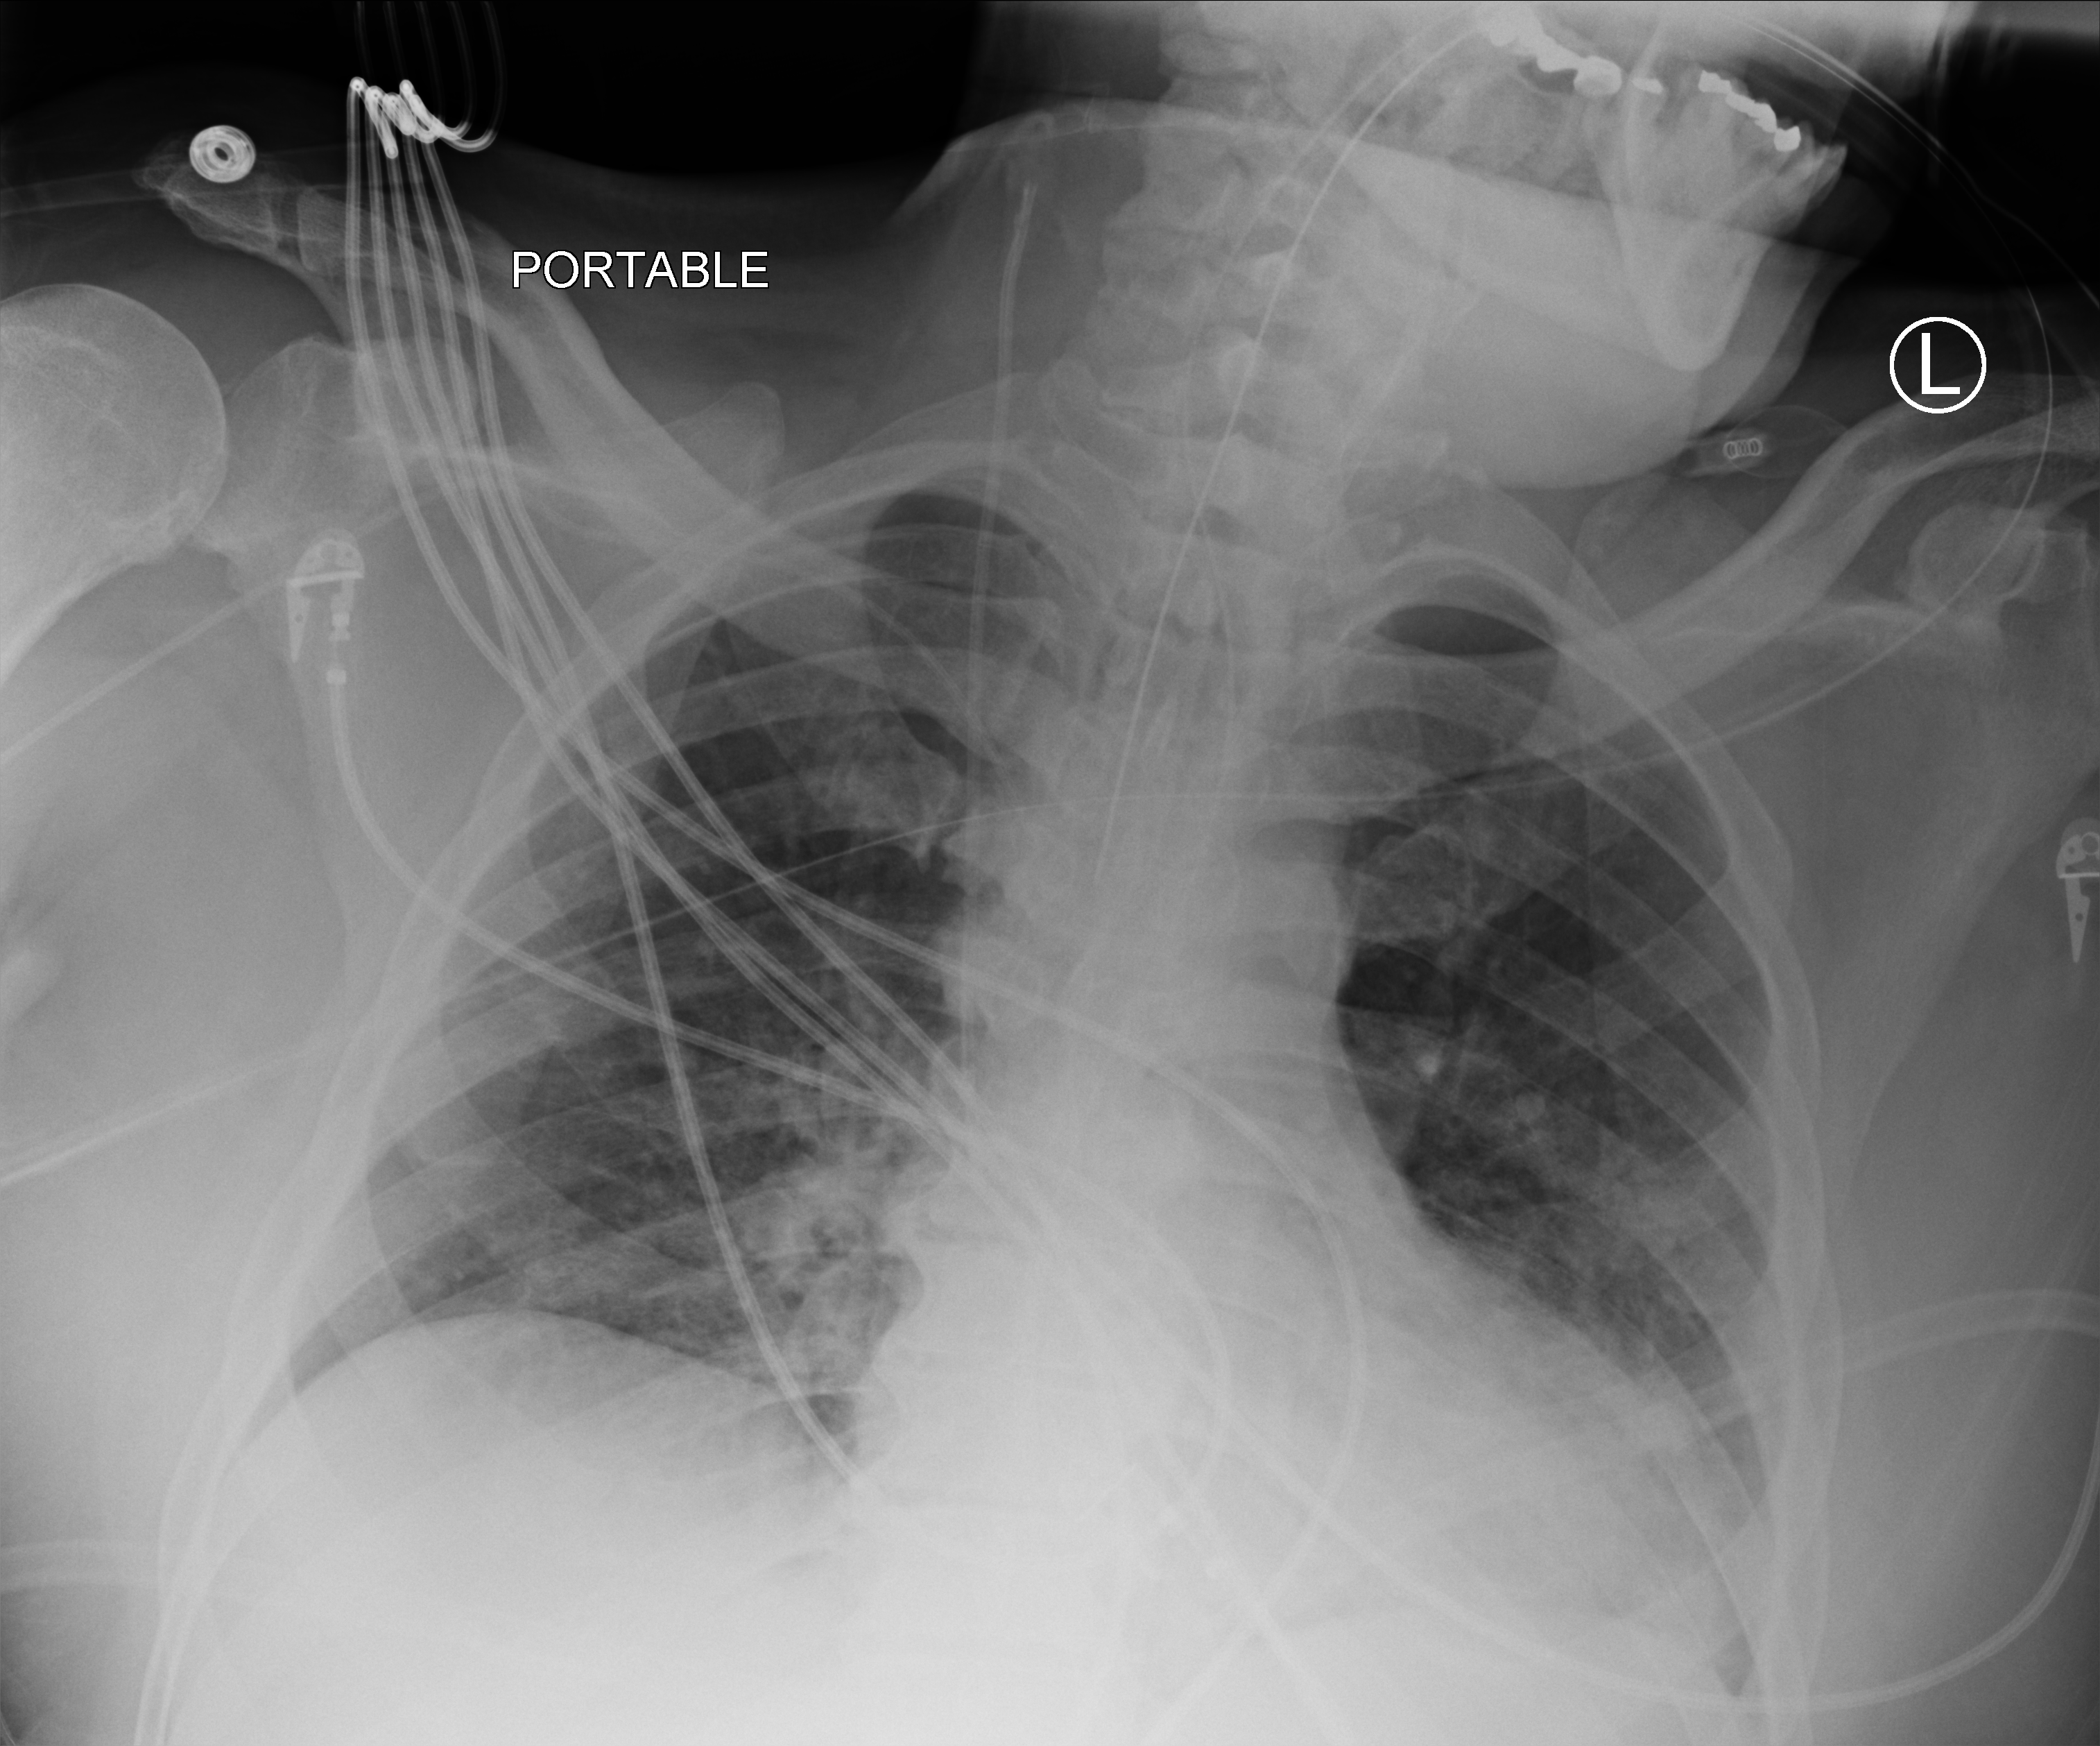
Portable chest radiograph; anteroposterior (AP) projection. Patient hospitalised with COVID-19; male, aged 18–59 years.
From the hospital-stay record, not from the radiograph (when in the stay this image was taken is not recorded):
- smoking status (admission record): never
- chronic kidney disease (admission record): no